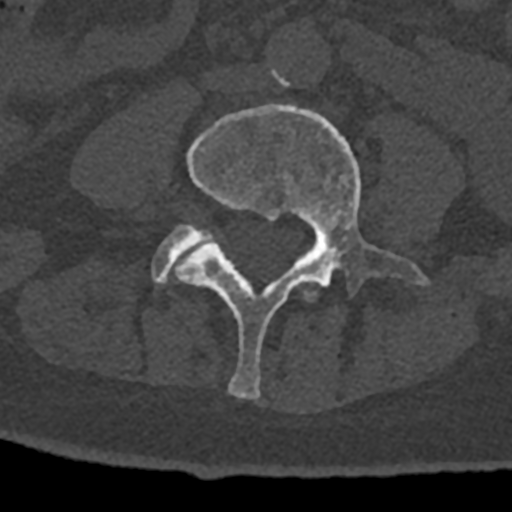
CT including the spine, one axial slice. Position 252 of 797 along the scan axis. 120 kVp. Bone window (W 1800 / L 400 HU). 0.5 mm slice thickness. 512 × 512 image matrix, field of view 160 × 160 mm. Patient: male, 74 years. From the clinical record (not read from this slice): primary cancer: renal; vertebrae with lytic lesions (as recorded): T10, L1, L2, L3, L4, L5.
Outlined on this slice (semi-automatic segmentation, software-assisted and operator-edited):
- L3 vertebra: box from (x=304, y=290) to (x=317, y=301) px
- L4 vertebra: (x=176, y=105)–(x=429, y=400)
- L5 vertebra: (x=152, y=224)–(x=211, y=284)